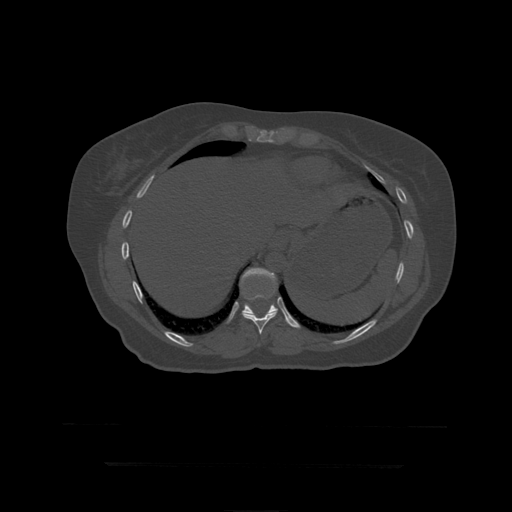
CT including the spine, one axial slice; 120 kVp; bone window (W 1800 / L 400 HU); 1.25 mm slice thickness; 512 × 512 image matrix, field of view 450 × 450 mm. Patient age 41 years. From the clinical record (not read from this slice): primary cancer: breast.
Outlined on this slice (semi-automatic segmentation, software-assisted and operator-edited):
- T10 vertebra: bounding box (x1, y1, x2, y2) in pixels: (242, 296, 278, 335)
- T11 vertebra: (241, 268, 278, 316)